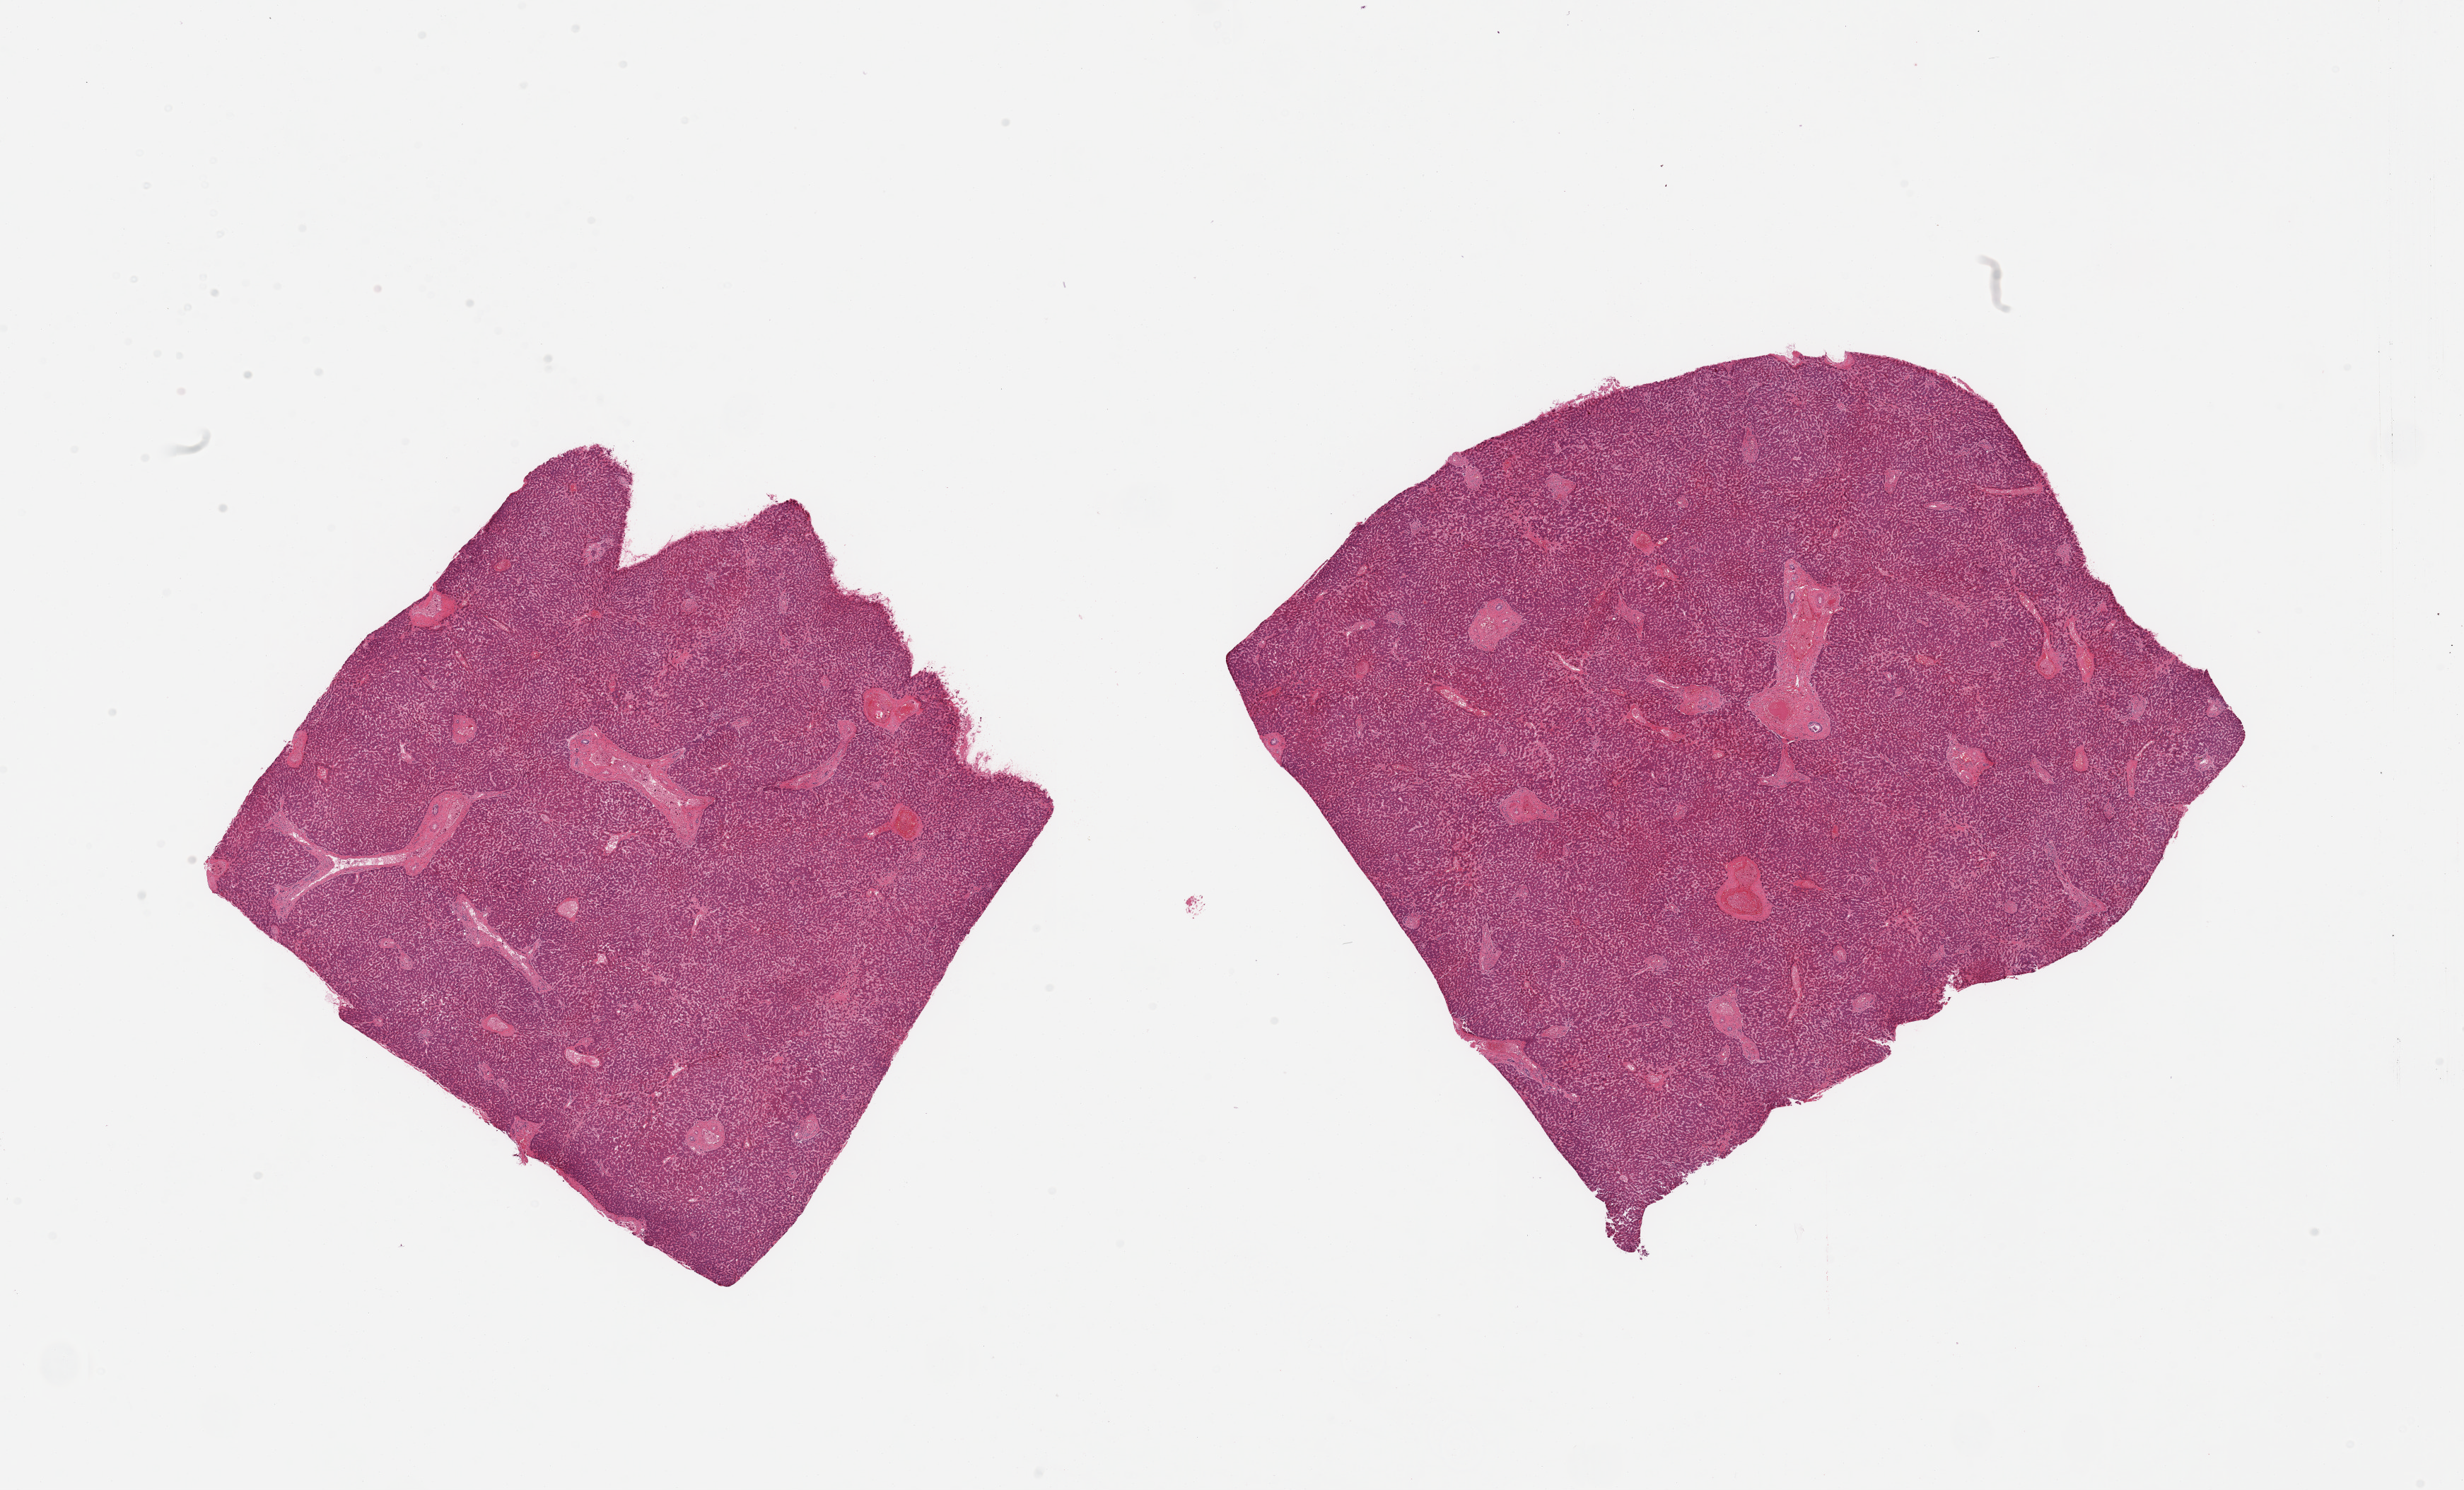
Whole-slide image, H&E stain, a low-resolution overview of the entire scanned area, about 27.6 x 16.7 mm (acquisition: 20x scan), PAXgene-fixed, paraffin-embedded tissue, sampled site (target tissue): liver, tissue donor sample.
Review note (as recorded): 2 pieces; no active or chronic lesions.